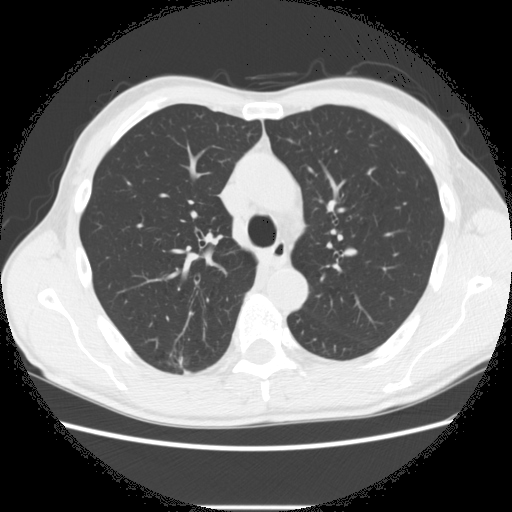
Low-dose screening chest CT, one axial slice. Slice 195 of 282 in the series (ordered by position). 120 kVp. Lung window (W 1500 / L -600 HU). 512 × 512 image matrix, field of view 360 × 360 mm.
Structures marked on this image (expert manual segmentation):
- lesion 1 (tumor, upper lobe of right lung): box from (x=177, y=357) to (x=188, y=372) px